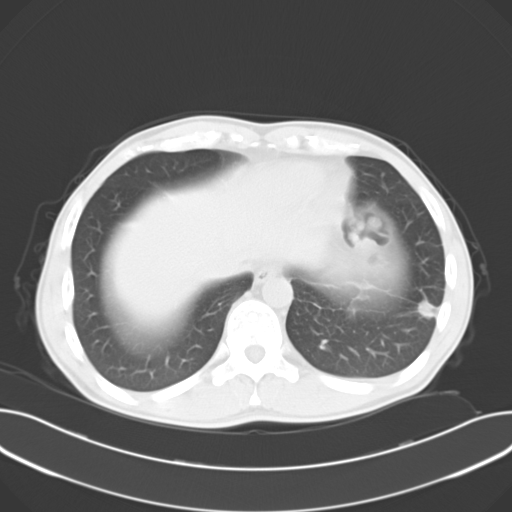
Chest CT, one axial slice. Slice 8 of 30 in the series (ordered by position). Reconstruction kernel B40f. 120 kVp. Lung window (W 1500 / L -600 HU). 10 mm slice thickness. 512 × 512 image matrix, field of view 374 × 374 mm. Patient: male, 44 years. From the clinical record (not read from this slice): clinical TNM (as recorded): T1c N0 M1b.
Structures marked on this image (bounding box drawn by a radiologist):
- lung tumour (recorded histology: adenocarcinoma): bounding box (x1, y1, x2, y2) in pixels: (415, 295, 443, 324)